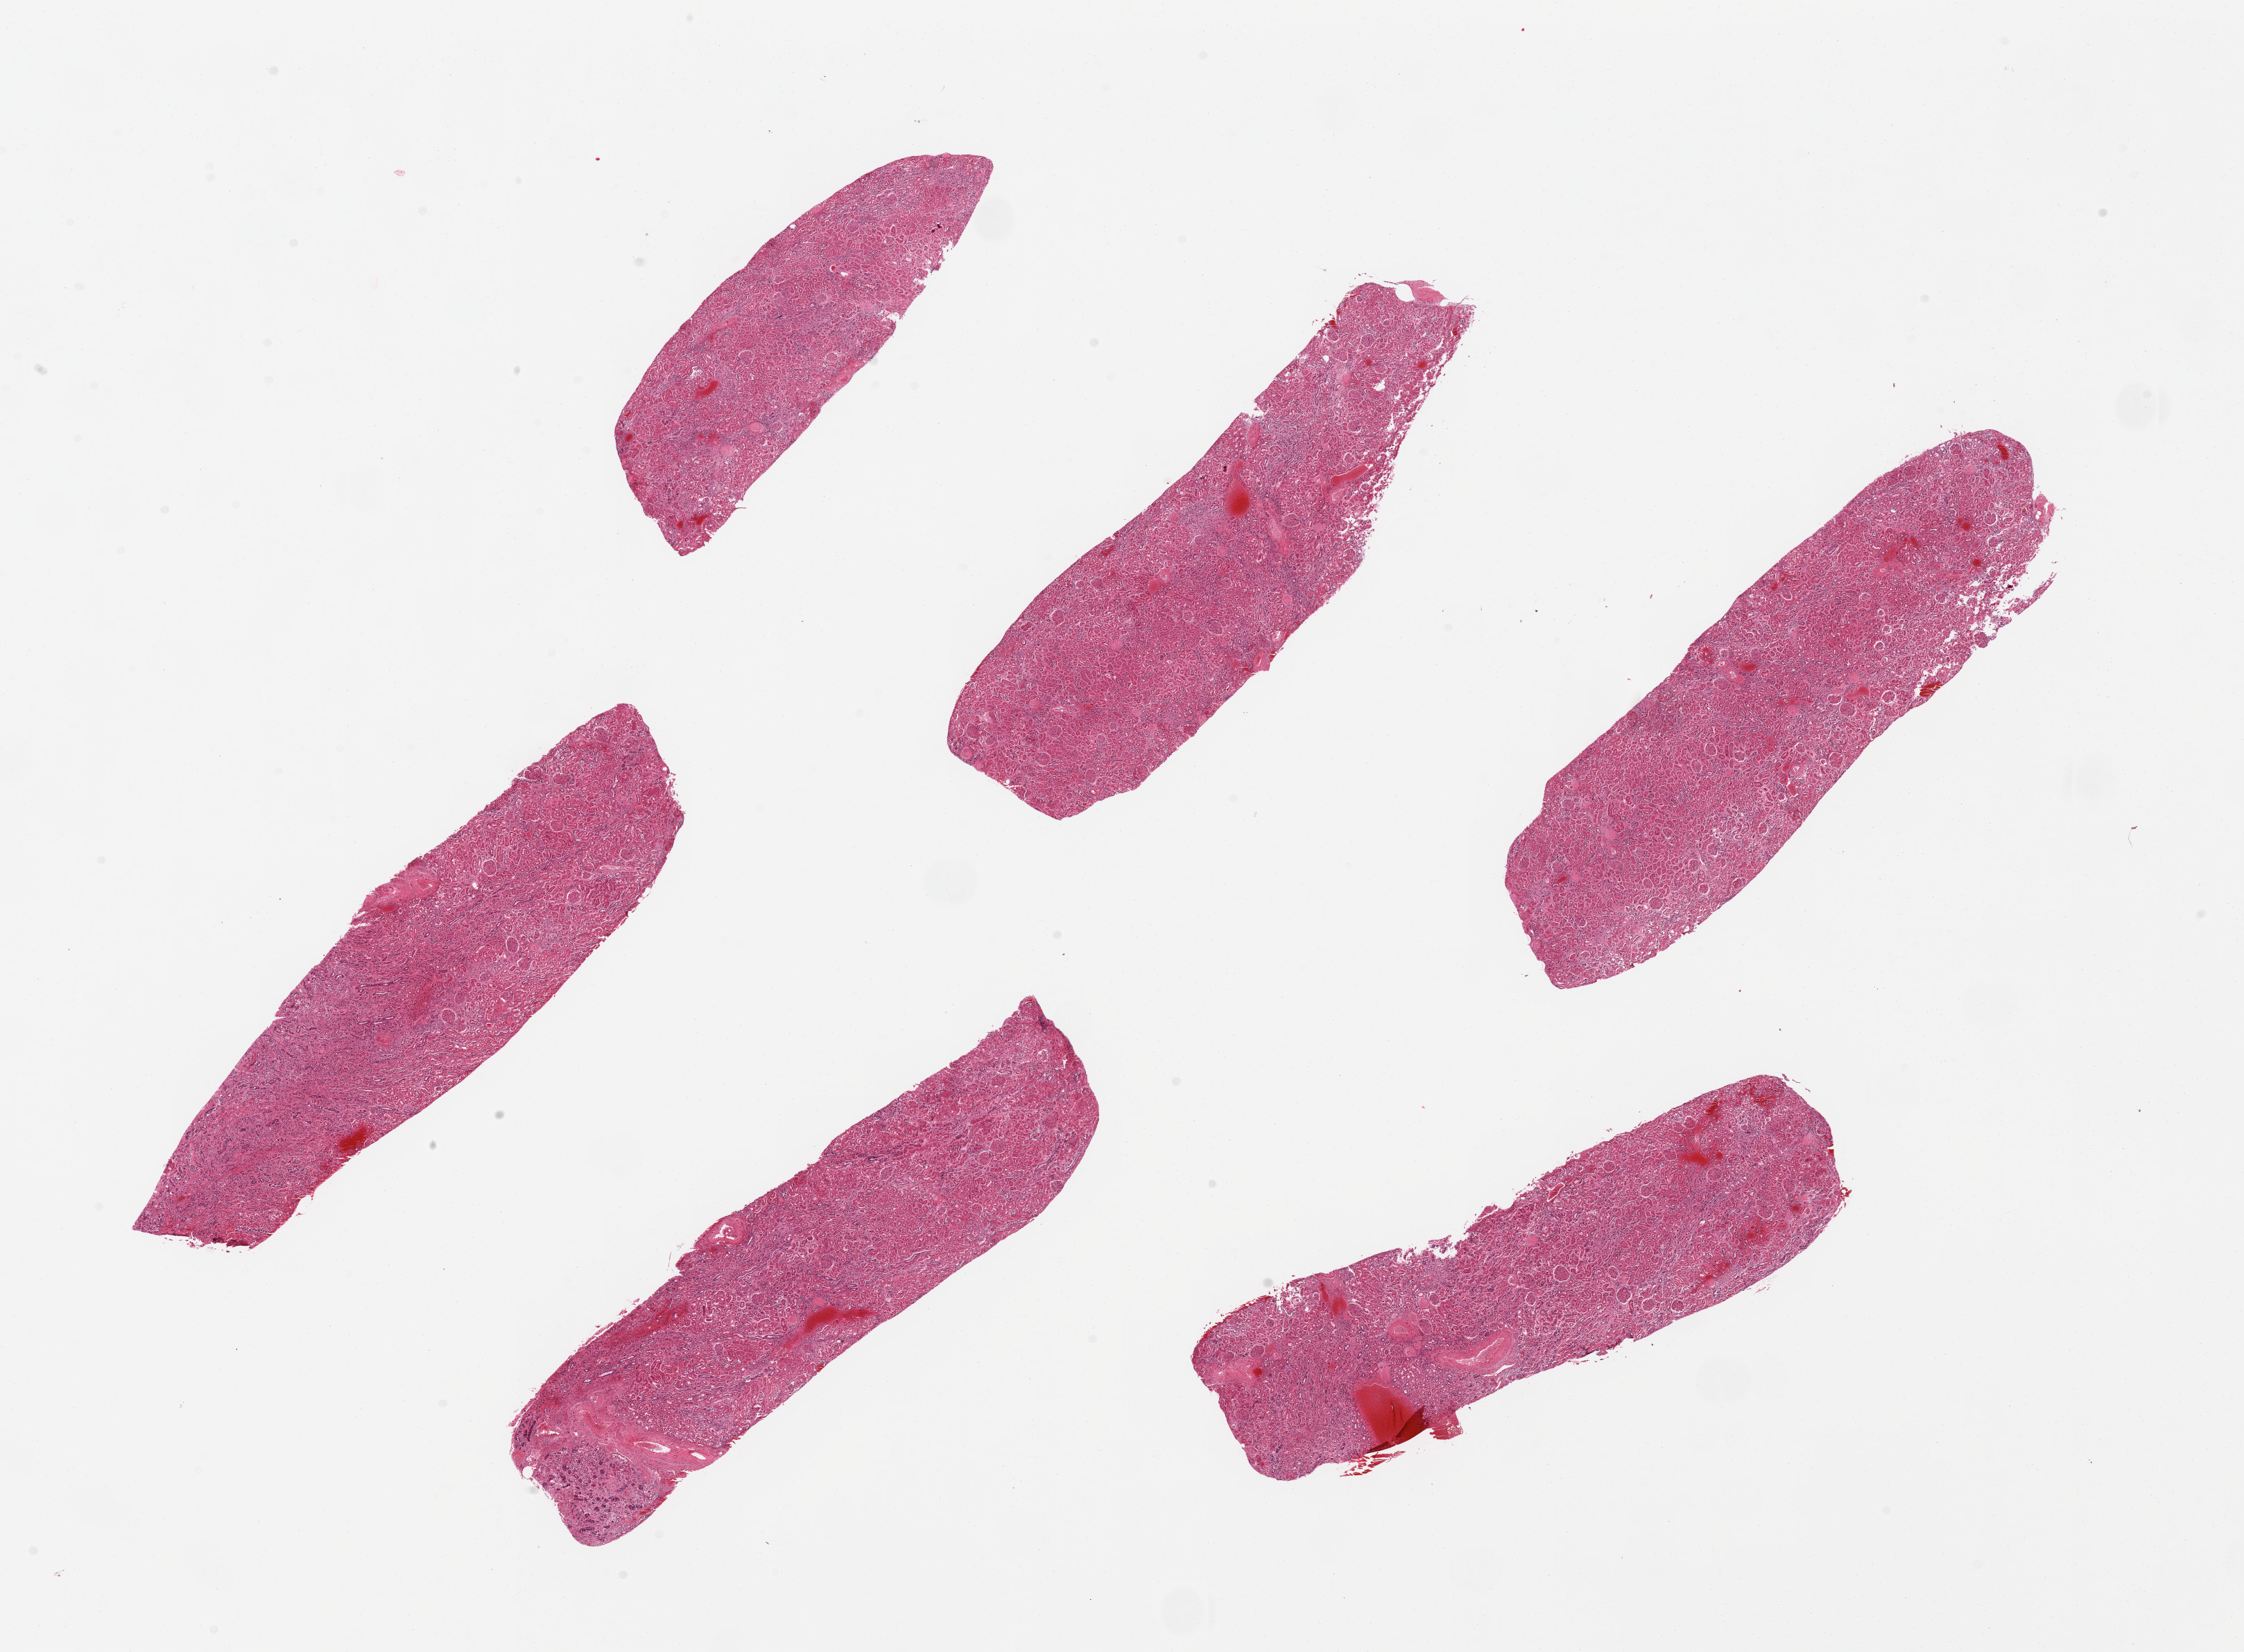
Haematoxylin and eosin whole-slide image, shown as a low-resolution overview of the whole scanned area (about 25.6 x 18.8 mm, from a 20x scan); PAXgene-fixed paraffin-embedded (PFPE) section; target tissue: renal cortex; donor tissue sample. Donor sex: female.
Pathologist's review note for this sample: 6 pieces, glomeruli present in all sections.